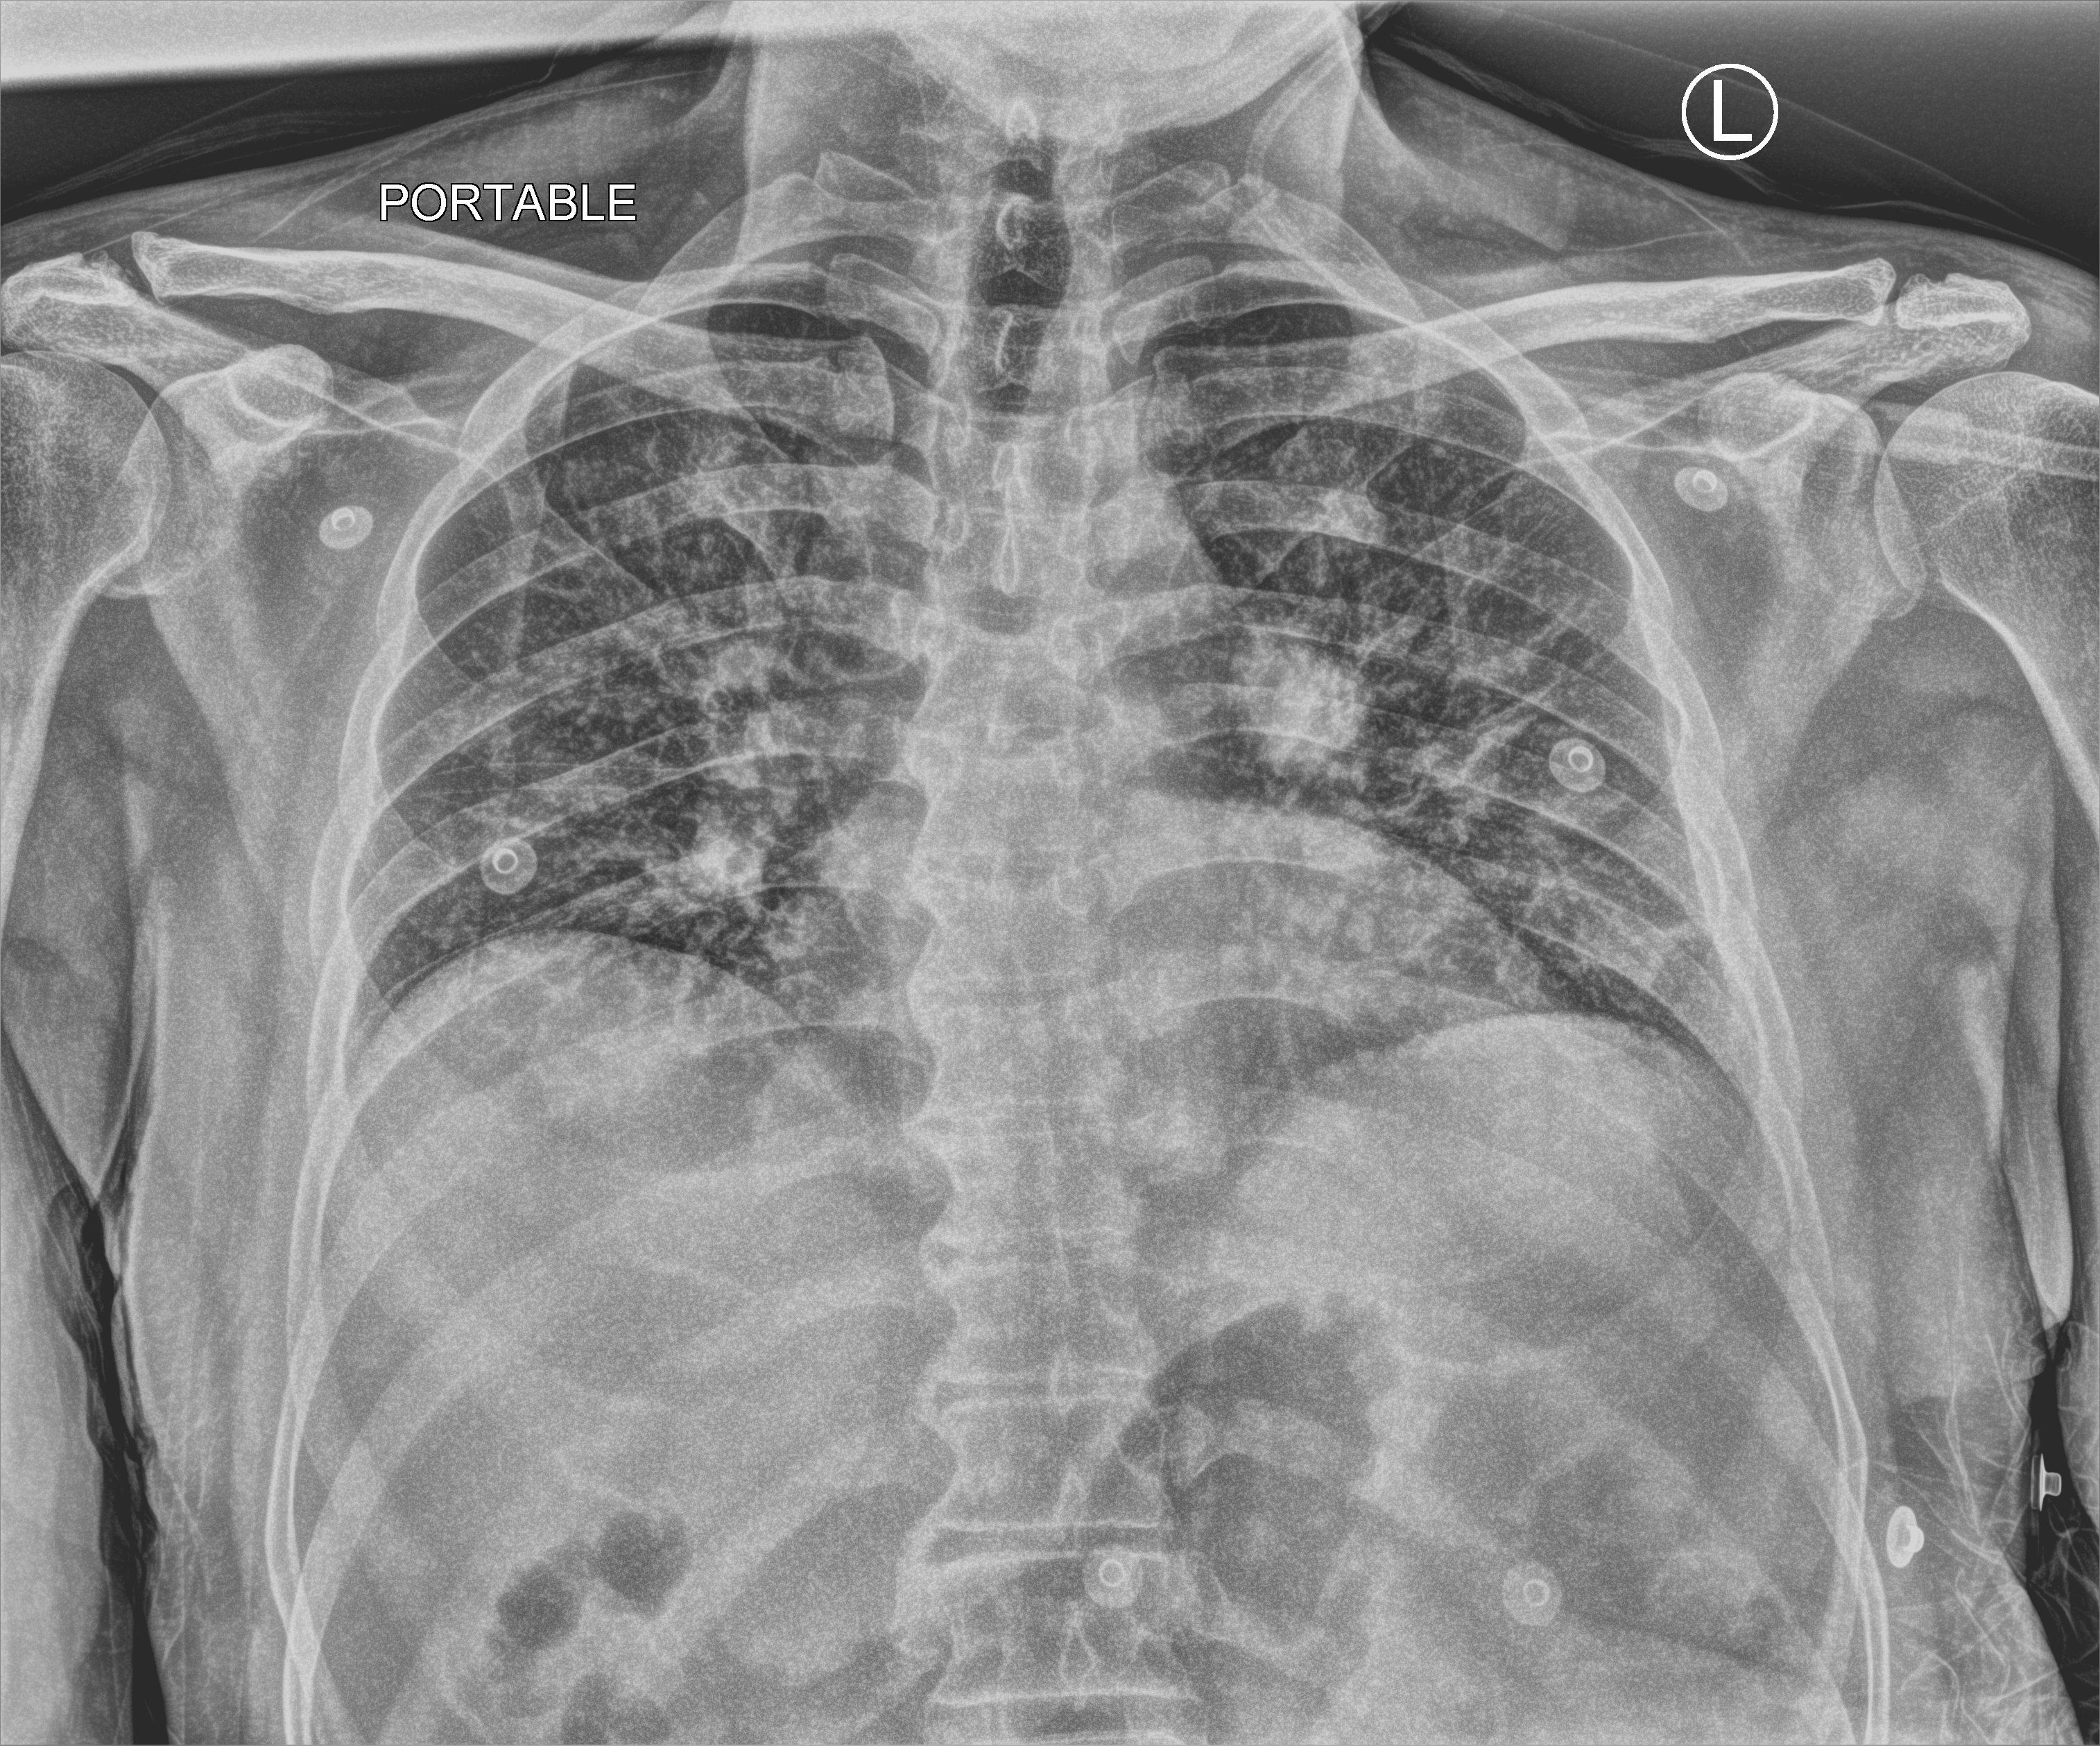
Portable chest radiograph, anteroposterior (AP) projection. Patient hospitalised with COVID-19; male, aged 18–59 years.
From the hospital-stay record, not from the radiograph (when in the stay this image was taken is not recorded): diabetes (admission record): no; admitted to intensive care during this hospital stay: no.